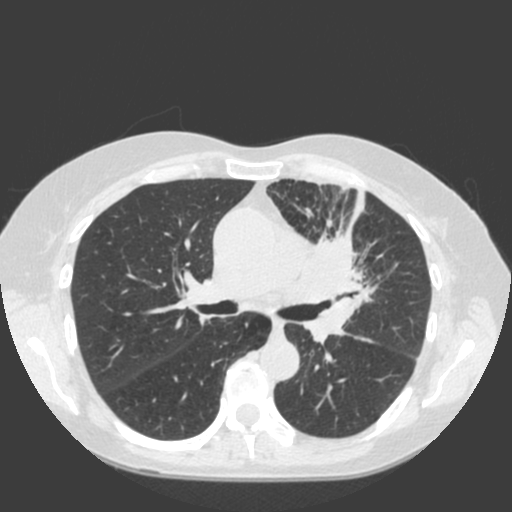
Chest CT (low-dose screening protocol), one axial image; first (baseline) screen; lung window (W 1500 / L -600 HU); 2 mm slice thickness; slice 69 of 184 in the series. Female, age 66 years at enrolment. Current smoker at enrolment.
• Lesion marked by an expert reader, bounding box <278,209,401,320> (left, top, right, bottom; pixels).
• The exam's reader record, not a measurement of the box and not confirmed to be the same lesion: non-calcified nodule or mass ≥4 mm, left upper lobe, 61 × 45 mm, spiculated (stellate) margins, soft tissue attenuation.
• Official screen result: positive, change unspecified: nodule(s) >= 4 mm or enlarging nodule(s), mass(es), or other non-specific abnormalities suspicious for lung cancer.
• Lung cancer was diagnosed 19 days after this screen: squamous cell carcinoma, keratinizing, NOS, left upper lobe, left hilum, mediastinum, left main stem bronchus, other location, poorly differentiated (G3), stage IIIB (AJCC 6th edition), 60 mm at pathology.